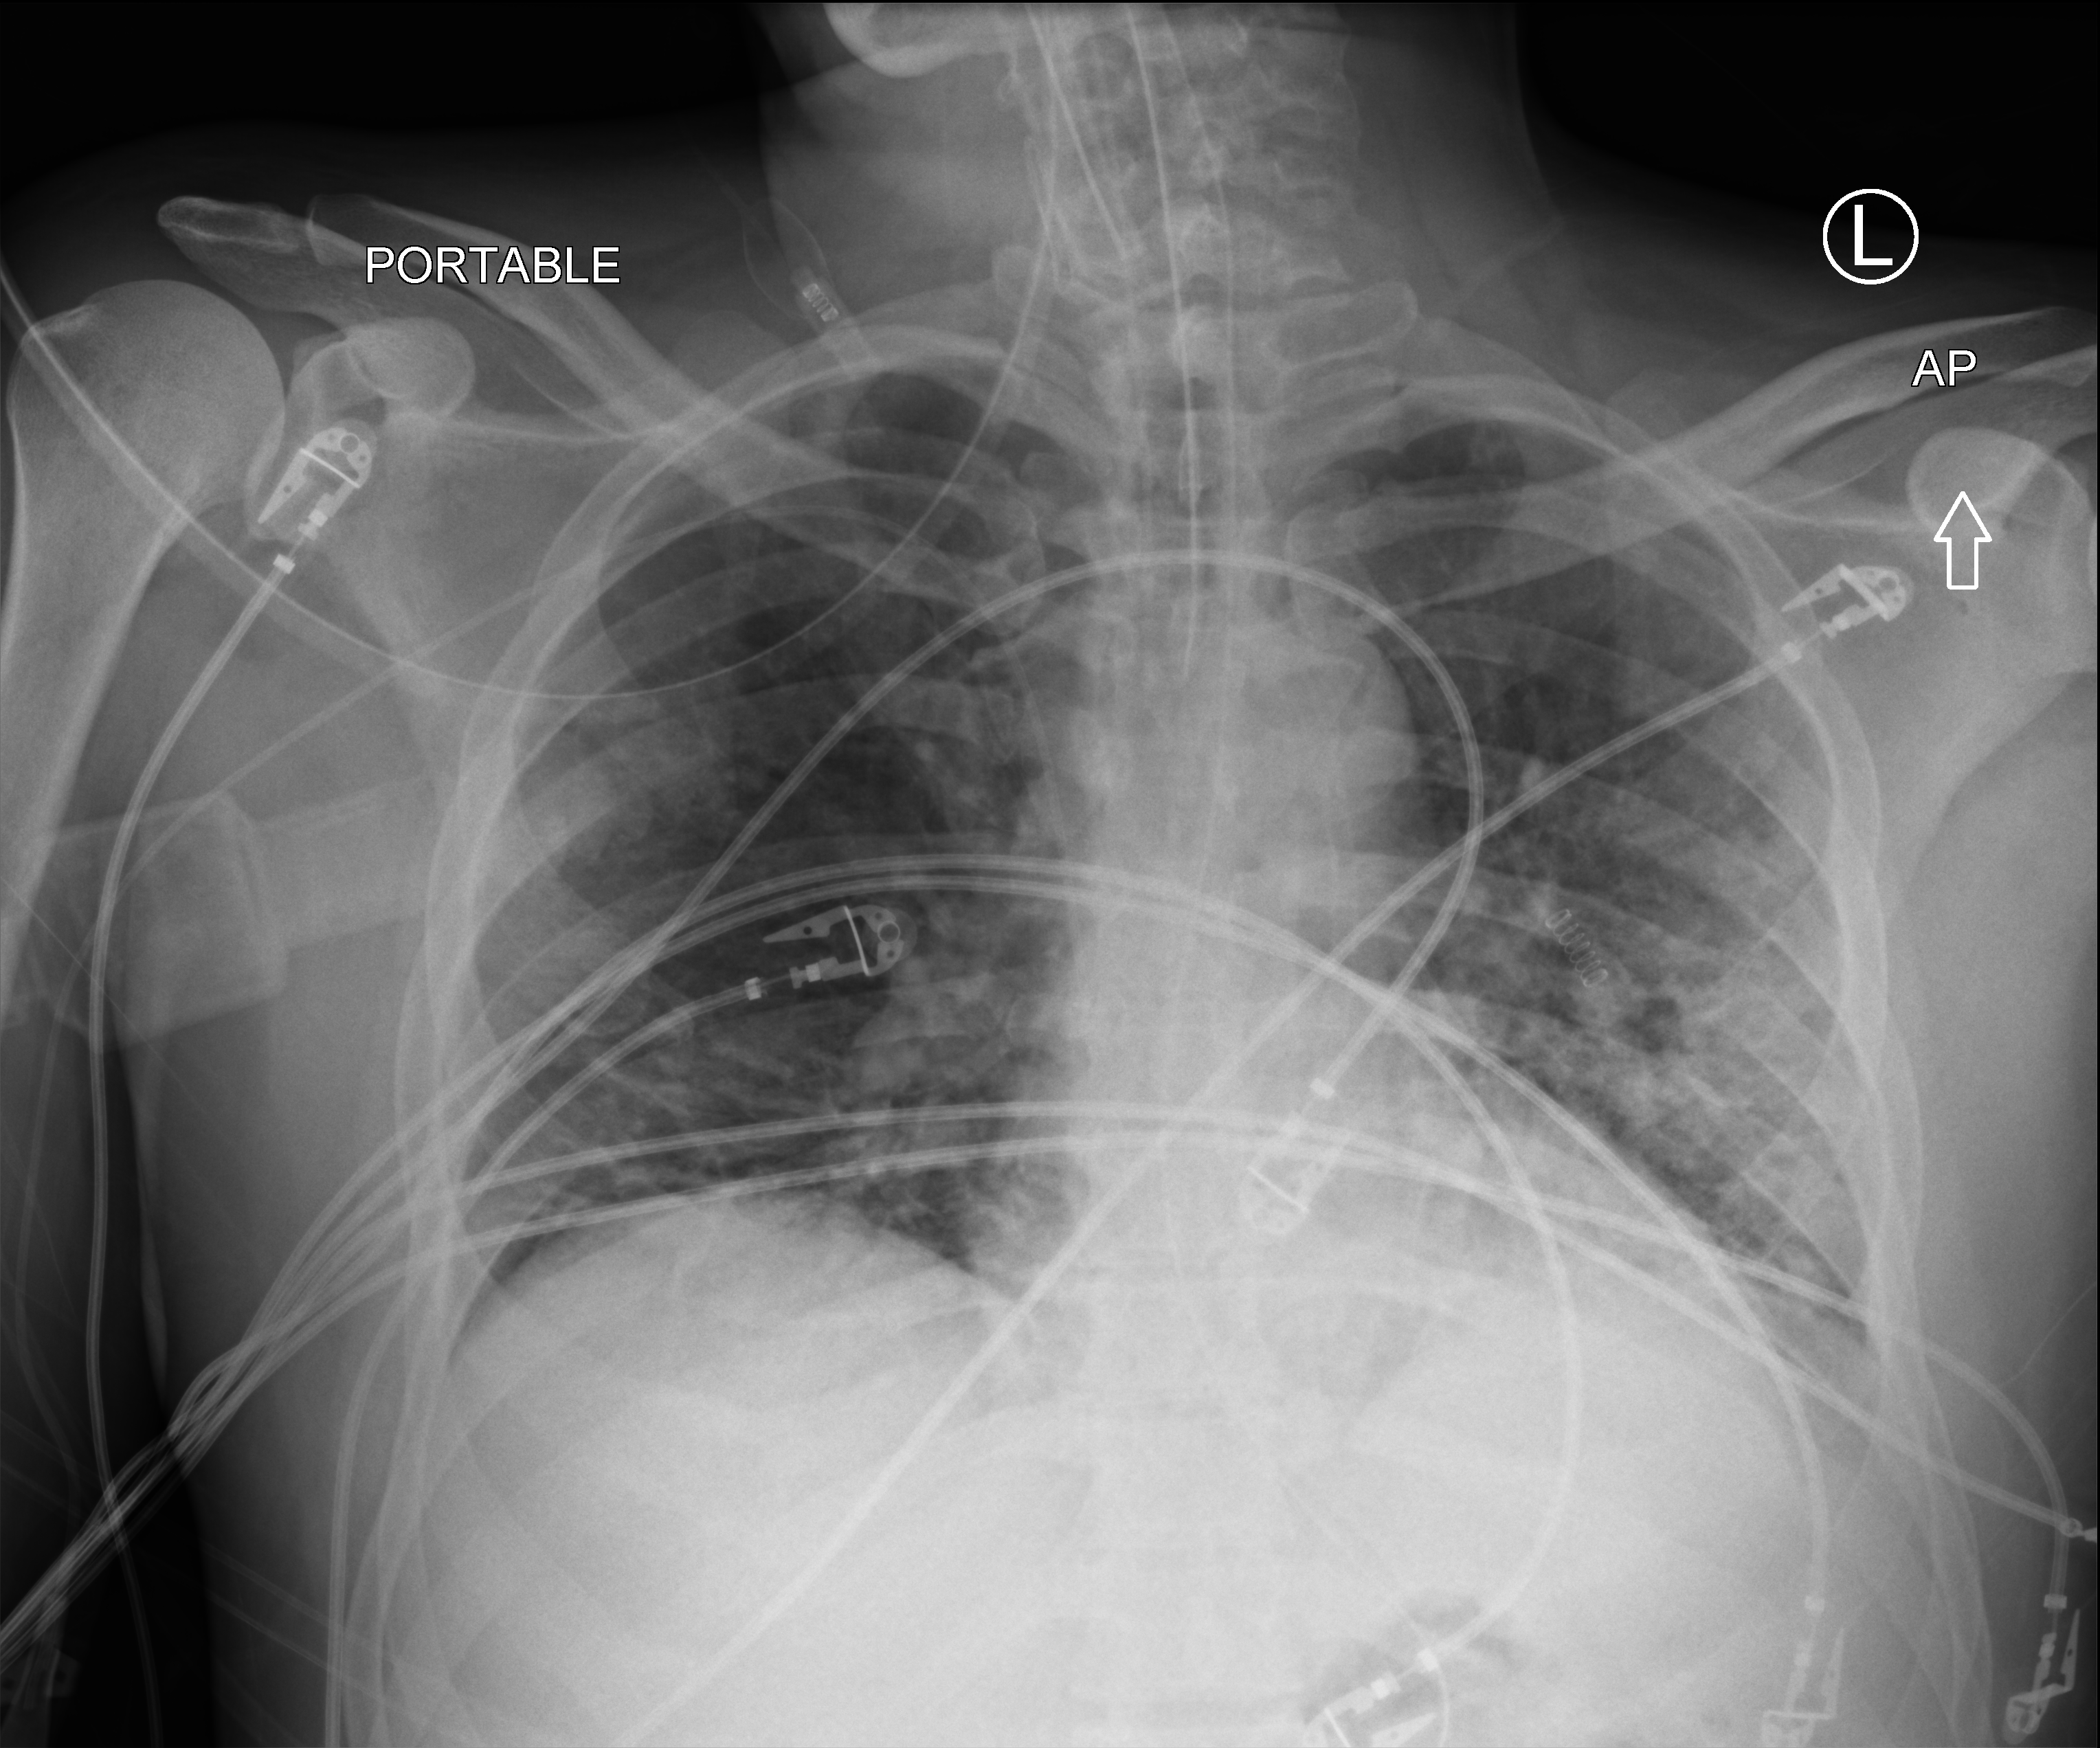
Bedside chest radiograph (computed radiography), anteroposterior (AP) projection. Male patient hospitalised with COVID-19, age 18–59 years.
Hospital-stay facts (about this admission, not read from this image; timing relative to this image not recorded):
- mechanically ventilated during this hospital stay: yes
- admitted to intensive care during this hospital stay: no
- chronic kidney disease (admission record): no